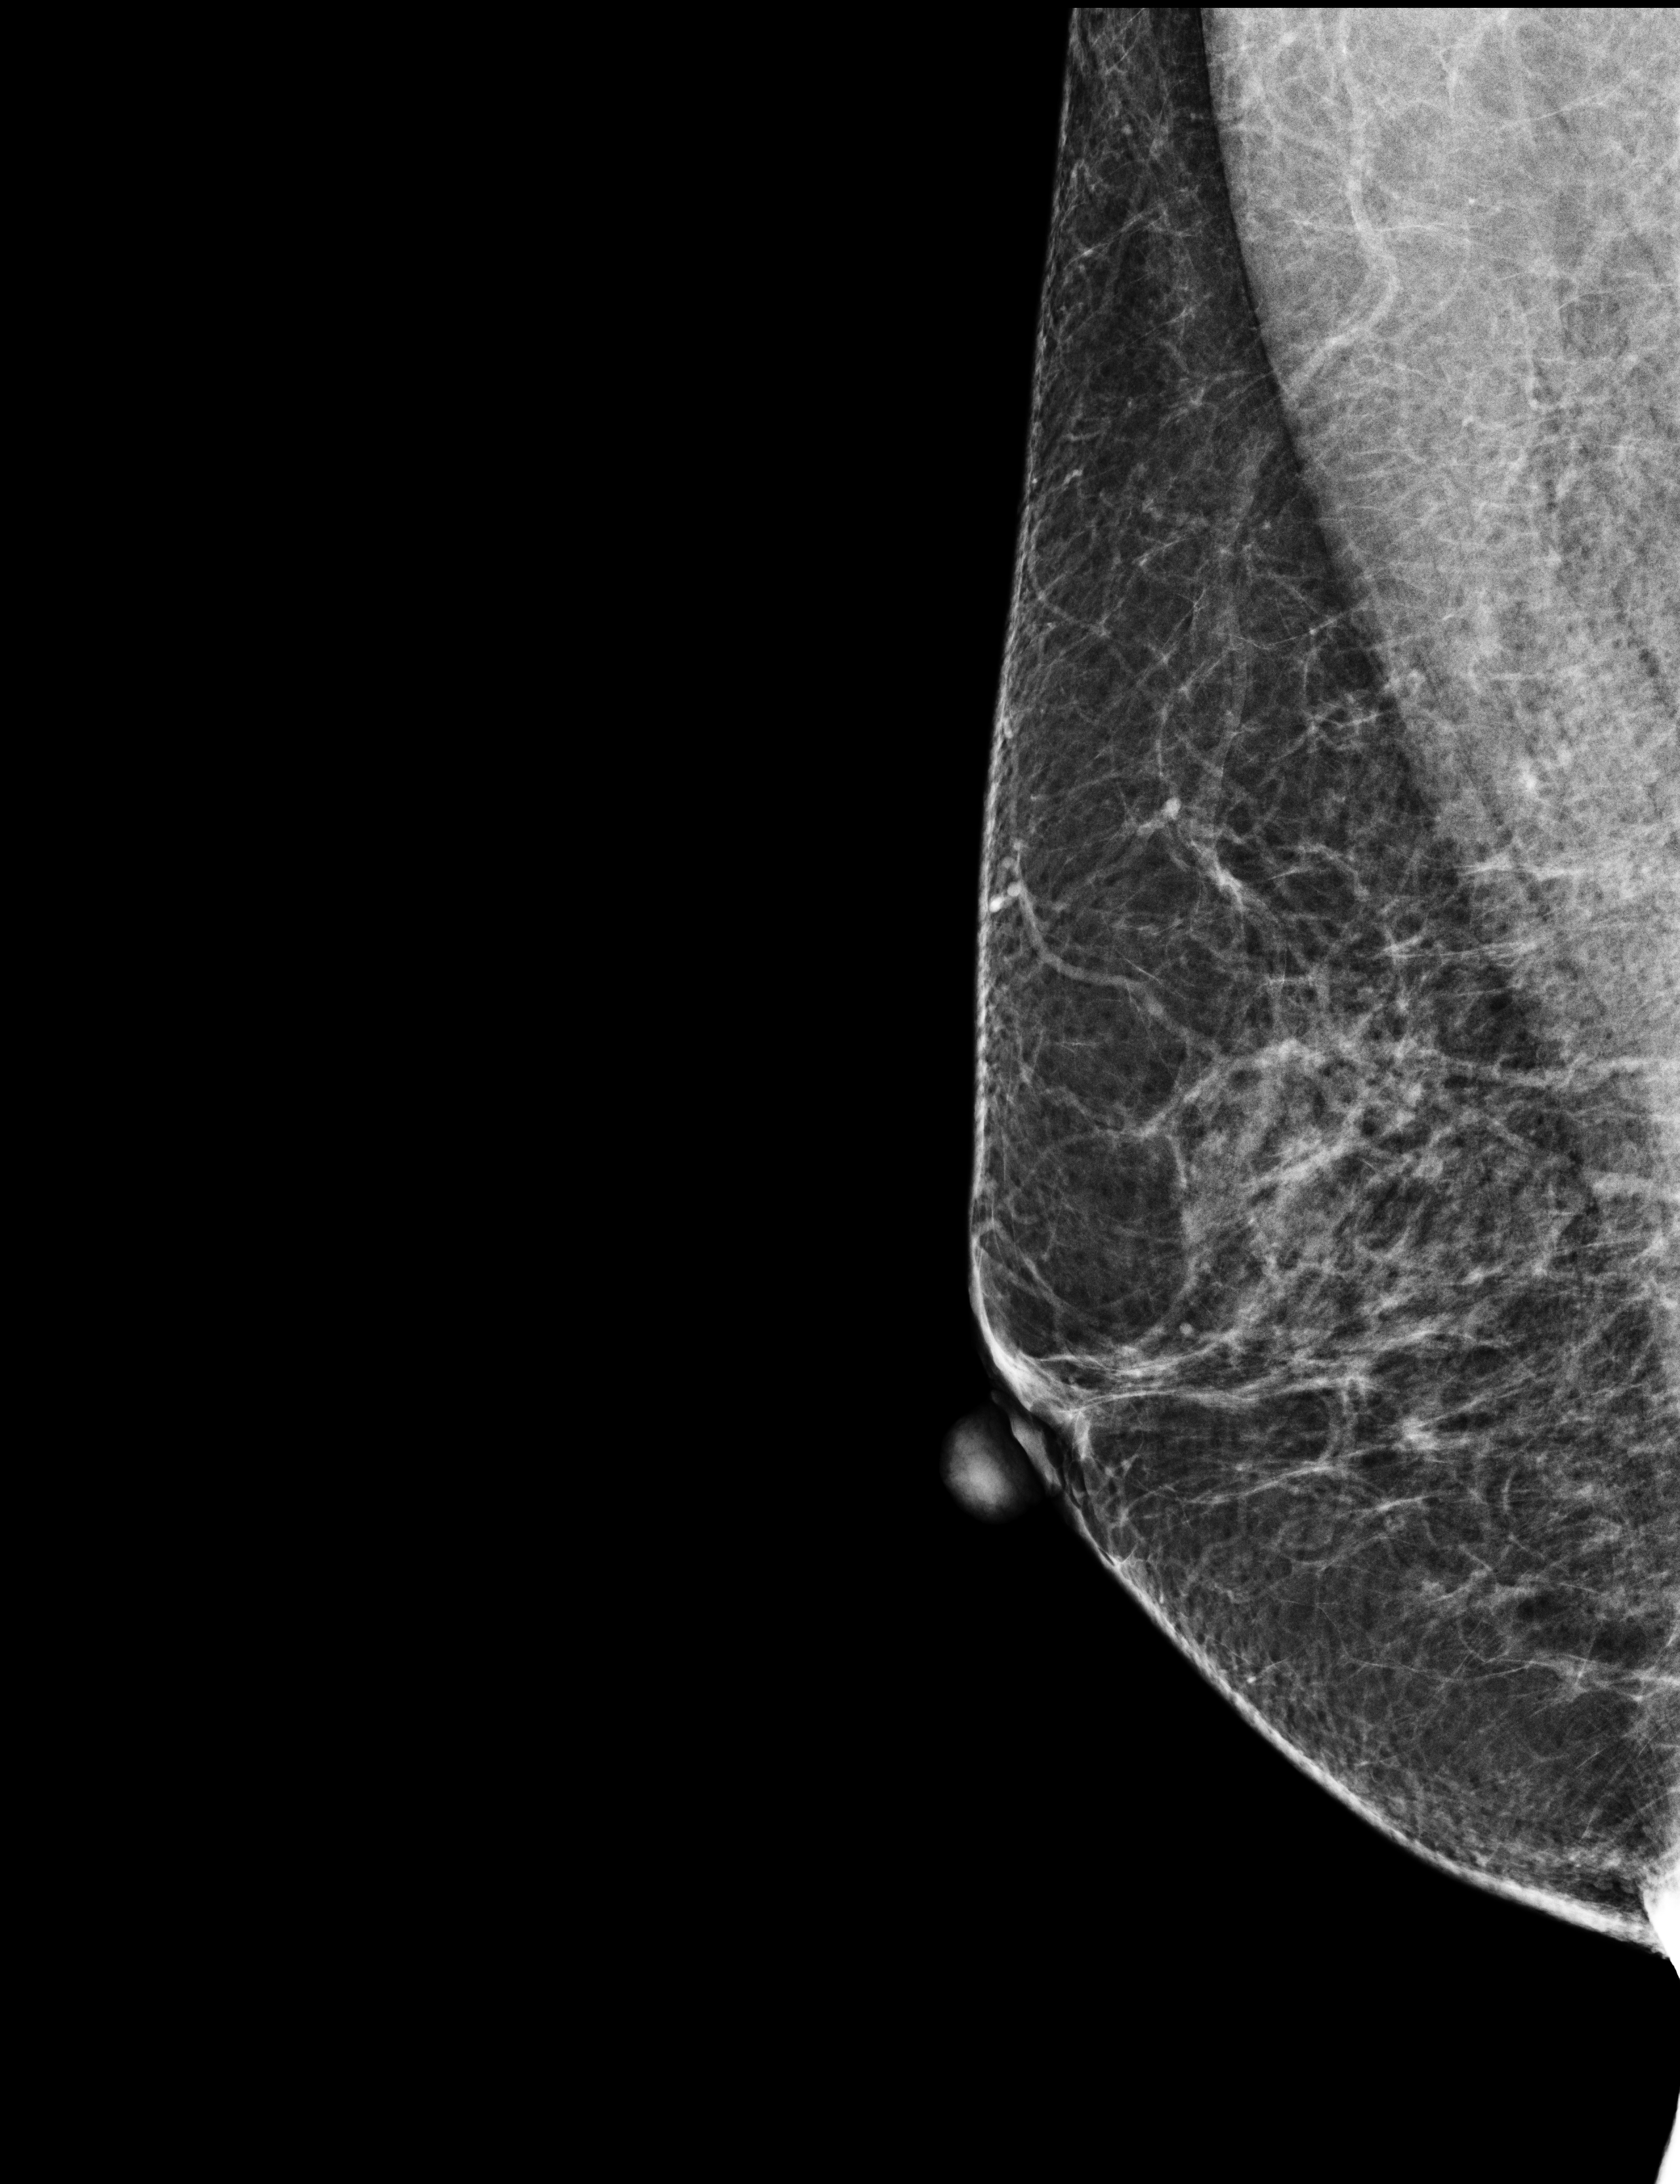
Digital mammogram (FFDM), right breast, mediolateral oblique (MLO) view, screening examination, compressed breast thickness 53 mm. Patient aged 61 years (female).
BI-RADS breast density category at the screening exam (both breasts, scale 1–4): 3. Final BI-RADS assessment for this screening round (tomosynthesis exam, both breasts): category 2. Recall: recalled for additional imaging after this screen.